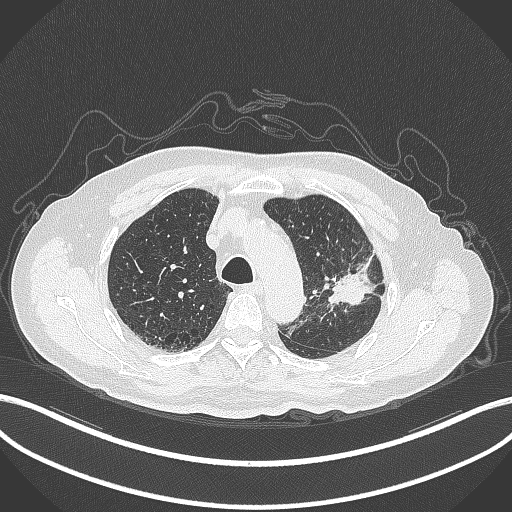
Chest CT, one axial slice. Position 225 of 331 along the scan axis. 120 kVp. Lung window (W 1500 / L -600 HU). 1 mm slice thickness. 512 × 512 image matrix. Male patient, age 79 years. From the clinical record (not read from this slice): clinical TNM (as recorded): T2a N1 M1.
Structures marked on this image (rectangle marked by the reading radiologist):
- lung tumour (recorded histology: adenocarcinoma): bounding box [x1, y1, x2, y2] px = [326, 252, 381, 310]